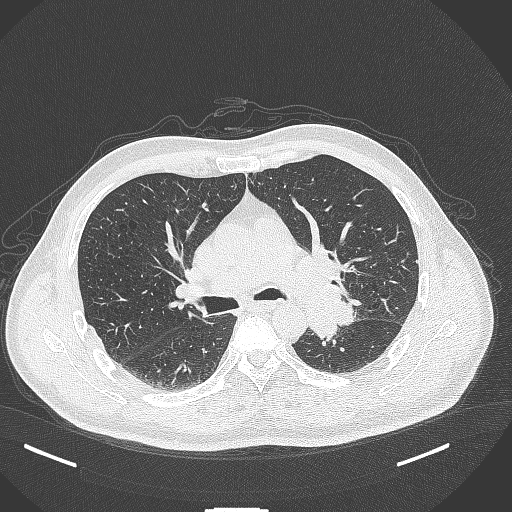
Chest CT, one axial slice; position 255 of 429 along the scan axis; reconstruction kernel B70f; 120 kVp; lung window (W 1500 / L -600 HU); 1 mm slice thickness; 512 × 512 image matrix, field of view 400 × 400 mm. Male patient, age 55 years. Case-level facts recorded for this patient, not image findings: clinical TNM (as recorded): T3 N0 M1c.
Structures marked on this image (rectangle marked by the reading radiologist):
- lung tumour (recorded histology: adenocarcinoma): bounding box [x1, y1, x2, y2] px = [304, 284, 363, 346]